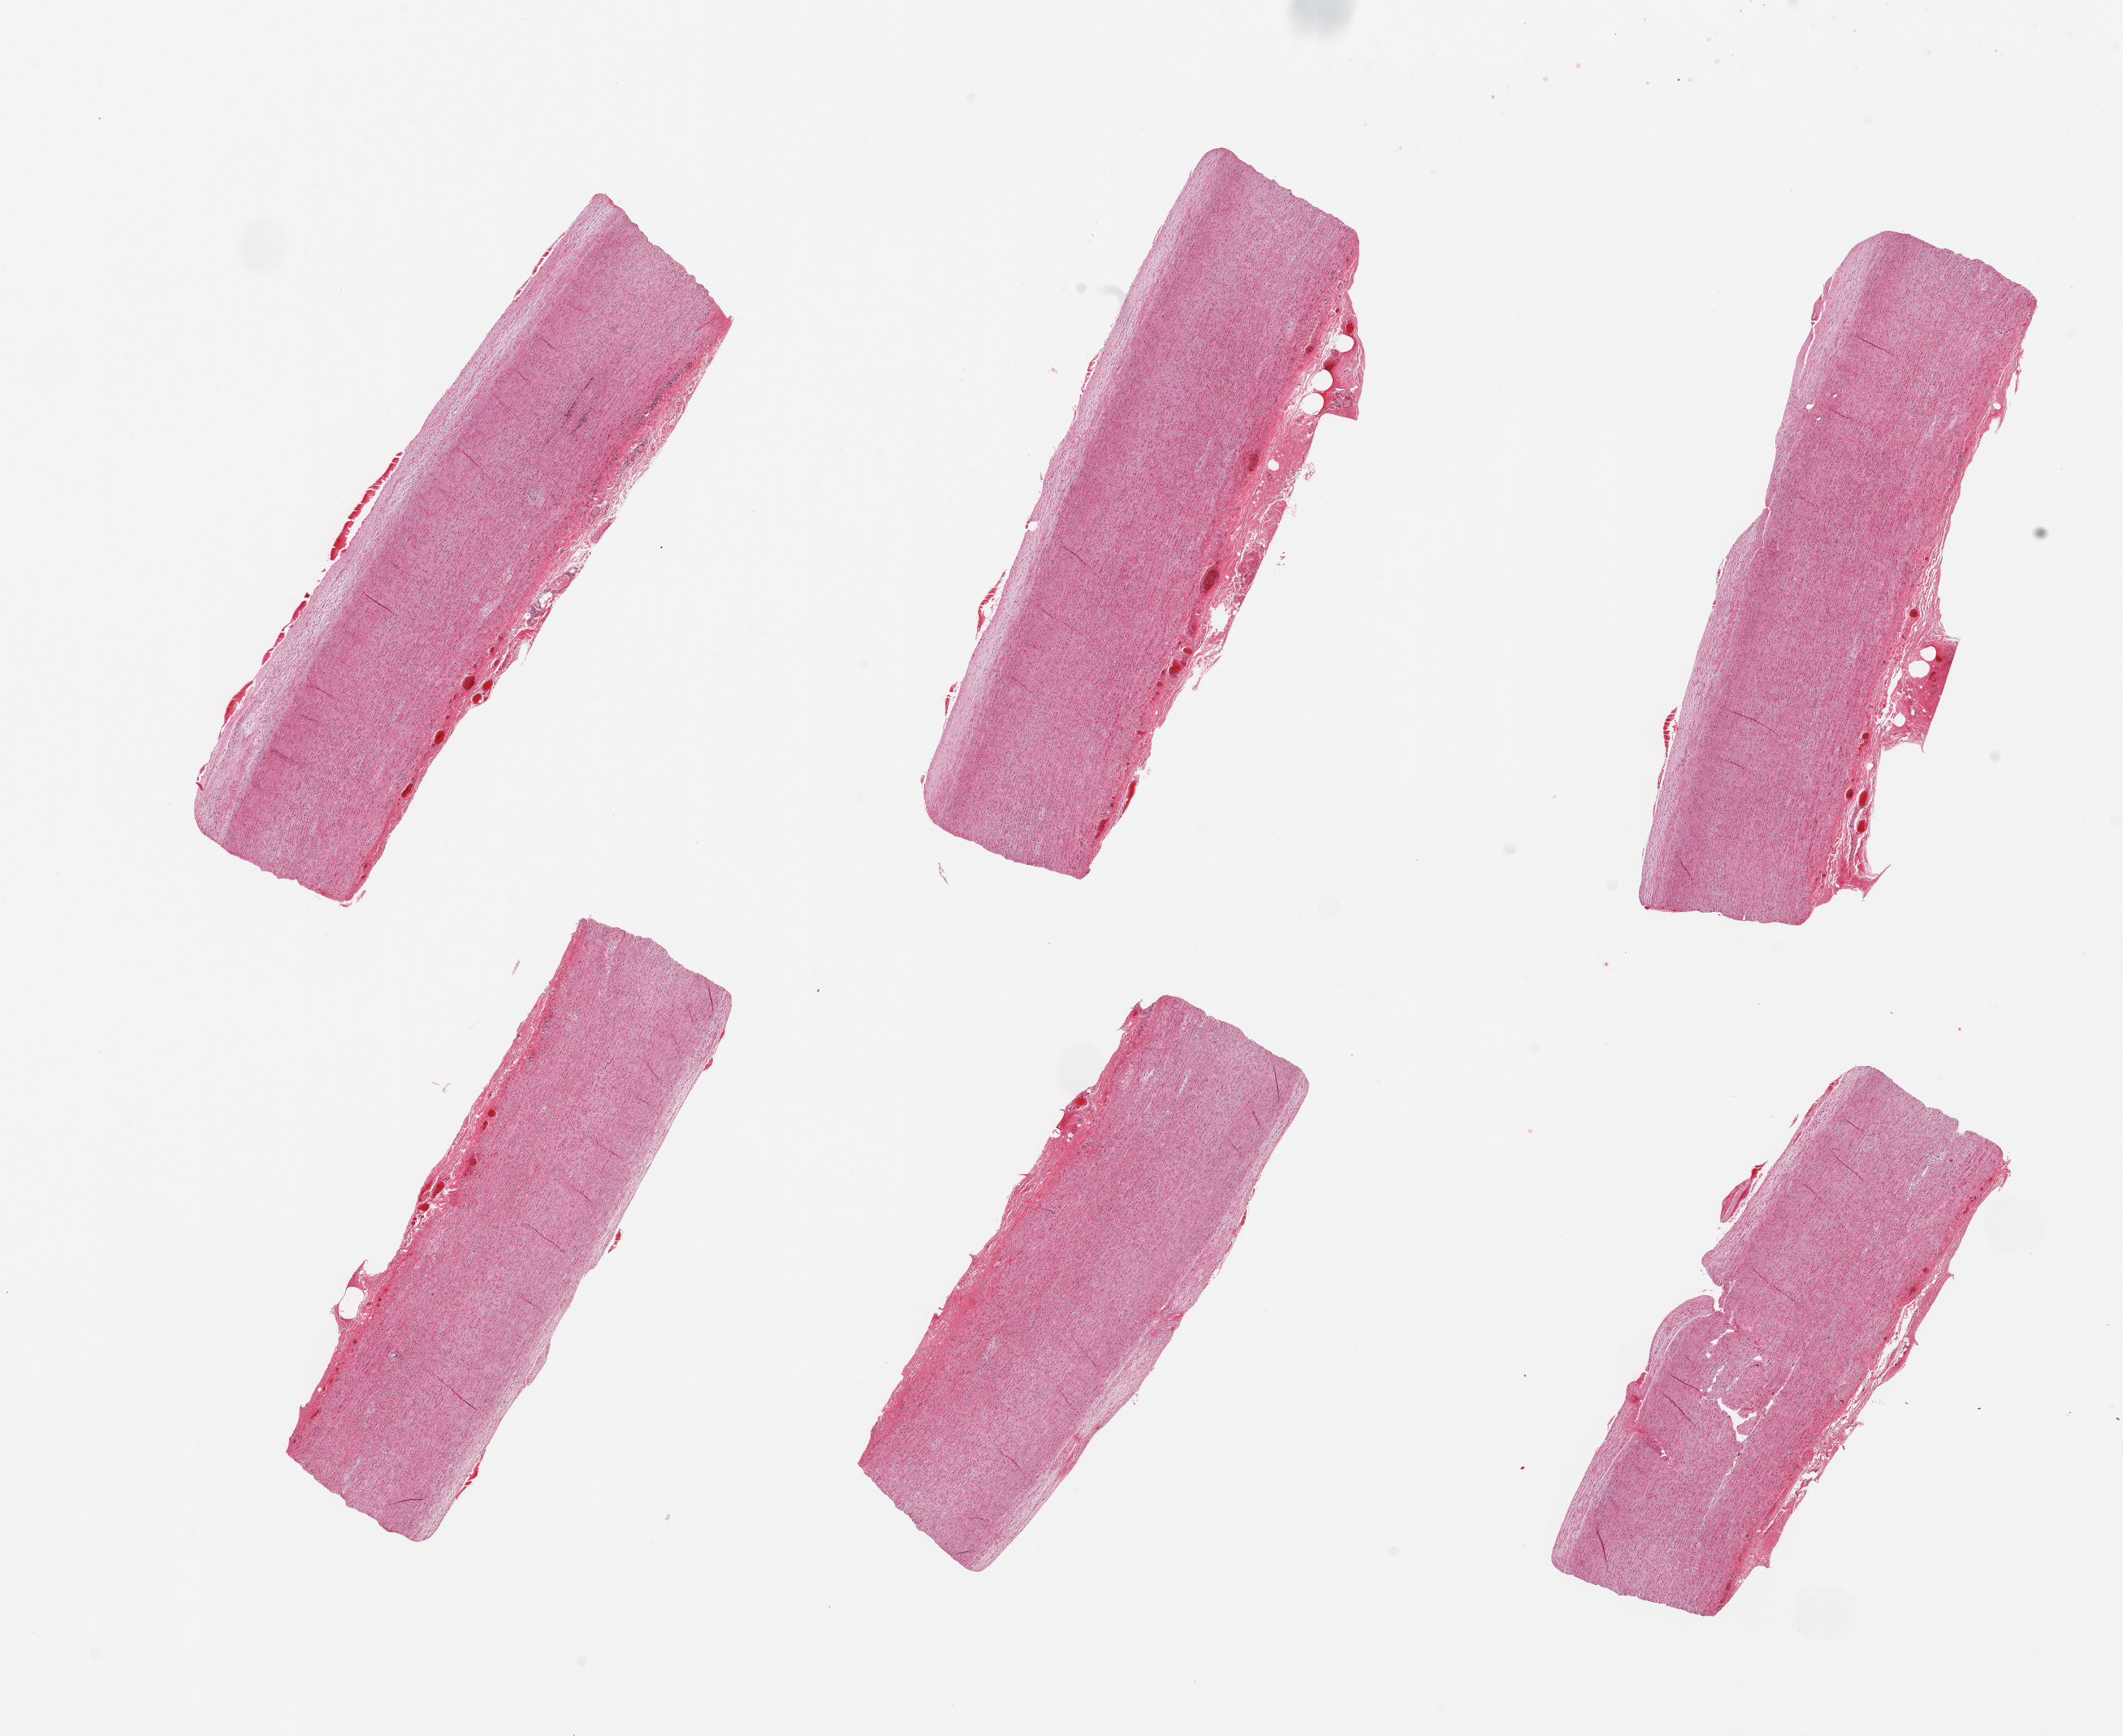
Hematoxylin and eosin (H&E) whole-slide image, low-resolution overview of the scanned area, about 20.7 x 16.9 mm; PAXgene-fixed paraffin-embedded (PFPE) section; sampled site (target tissue): aorta; tissue donor sample. Donor: female.
- reviewer comment on this tissue sample: 6 pieces, mild atherosis up to ~0.4mm